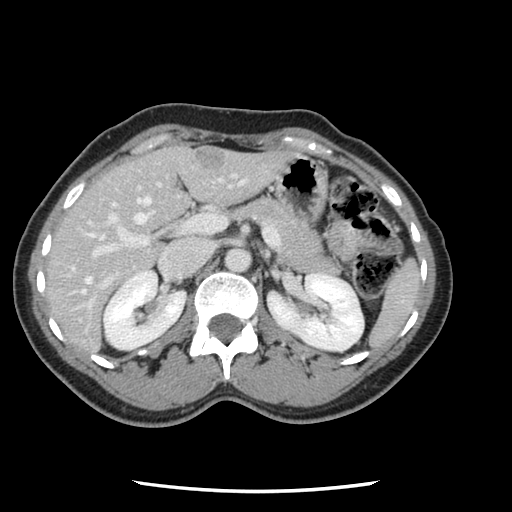
Contrast-enhanced abdominal CT, one axial slice; position 65 of 134 along the scan axis; 120 kVp; intravenous contrast given; soft-tissue window (W 400 / L 40 HU); 2.5 mm slice thickness; 512 × 512 image matrix, field of view 330 × 330 mm. Female patient, age 43 years. From the clinical record (not read from this slice): diagnosis: colorectal cancer liver metastases, imaged before liver resection; multiple liver metastases: yes.
Annotated regions visible in this slice (expert manual segmentation):
- hepatic veins: bounding box [x1, y1, x2, y2] px = [72, 180, 244, 294]
- liver: [46, 145, 291, 352]
- planned liver remnant (the part of the liver to remain after resection): [46, 150, 185, 306]
- portal vein (with intrahepatic branches): [74, 174, 277, 330]
- liver metastasis: [195, 153, 226, 170]